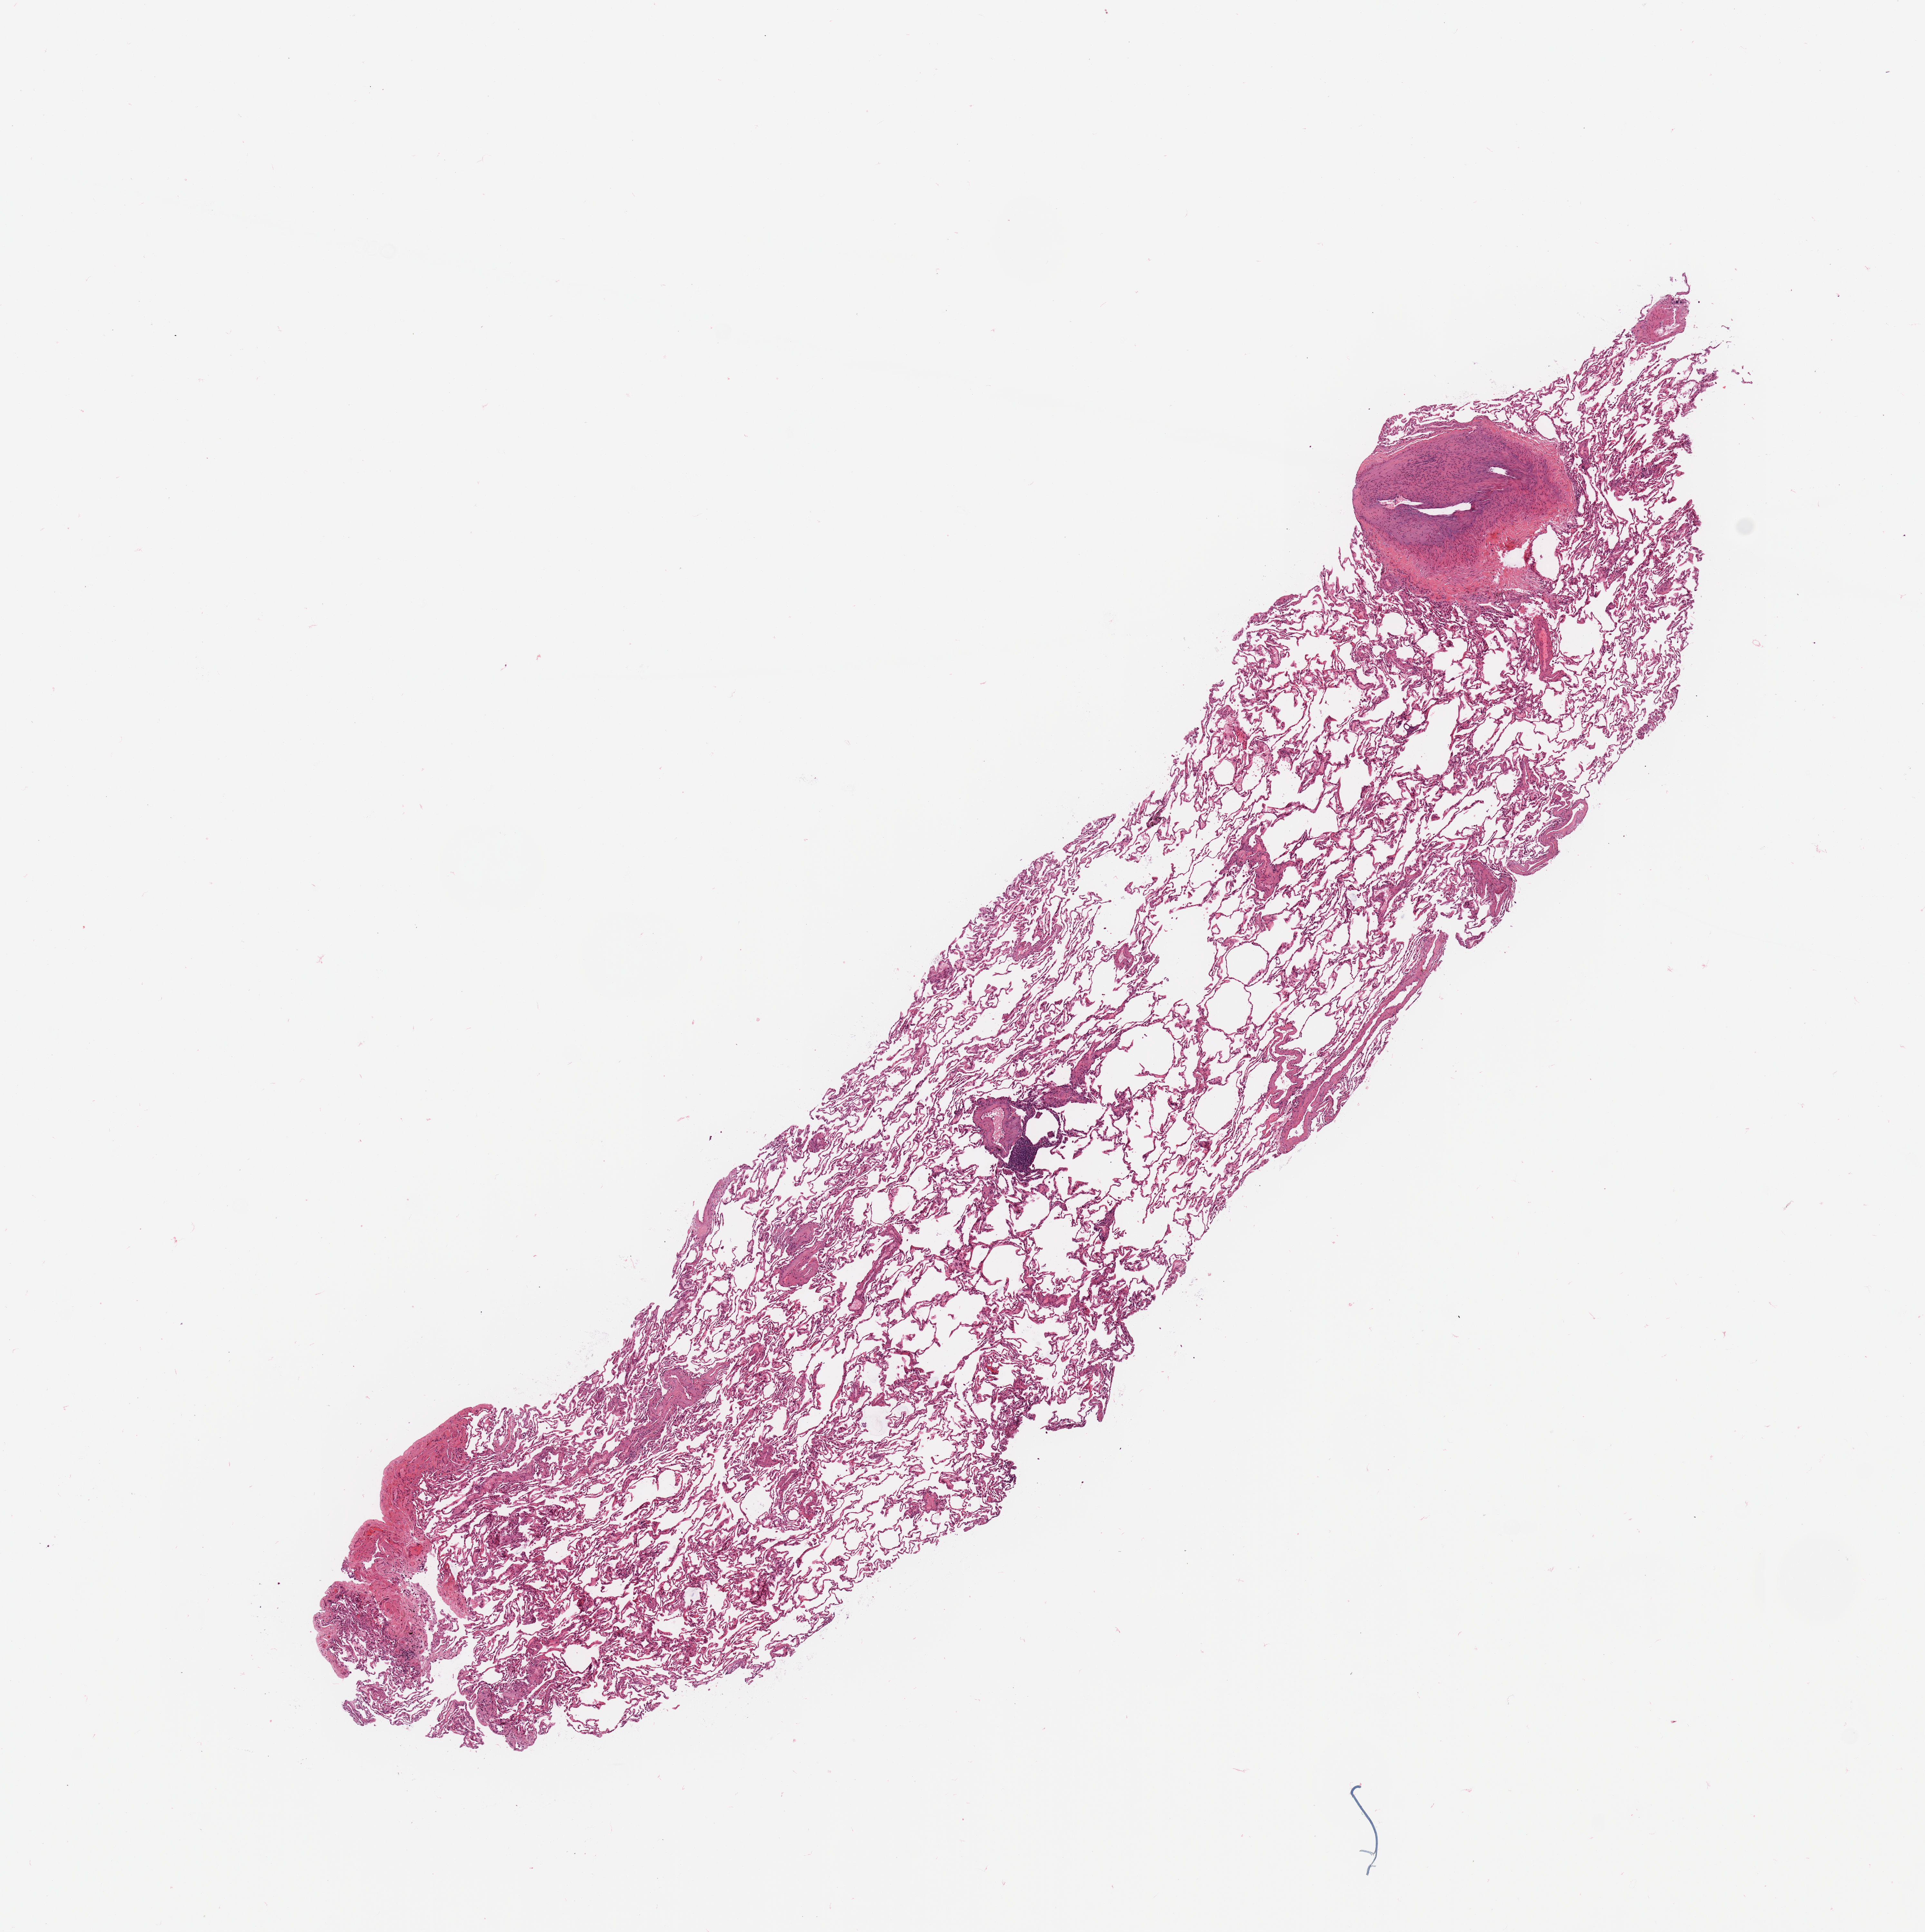
Hematoxylin and eosin (H&E) stained whole-slide image, whole scanned area (about 11.8 x 11.9 mm, acquisition: 20x scan) shown as a low-resolution overview, normal (non-tumour) tissue sample, sampled site: lung. Female, 70 y/o.
This section: normal (non-tumour) tissue from the same patient. Patient diagnosis: Adenocarcinoma, NOS.